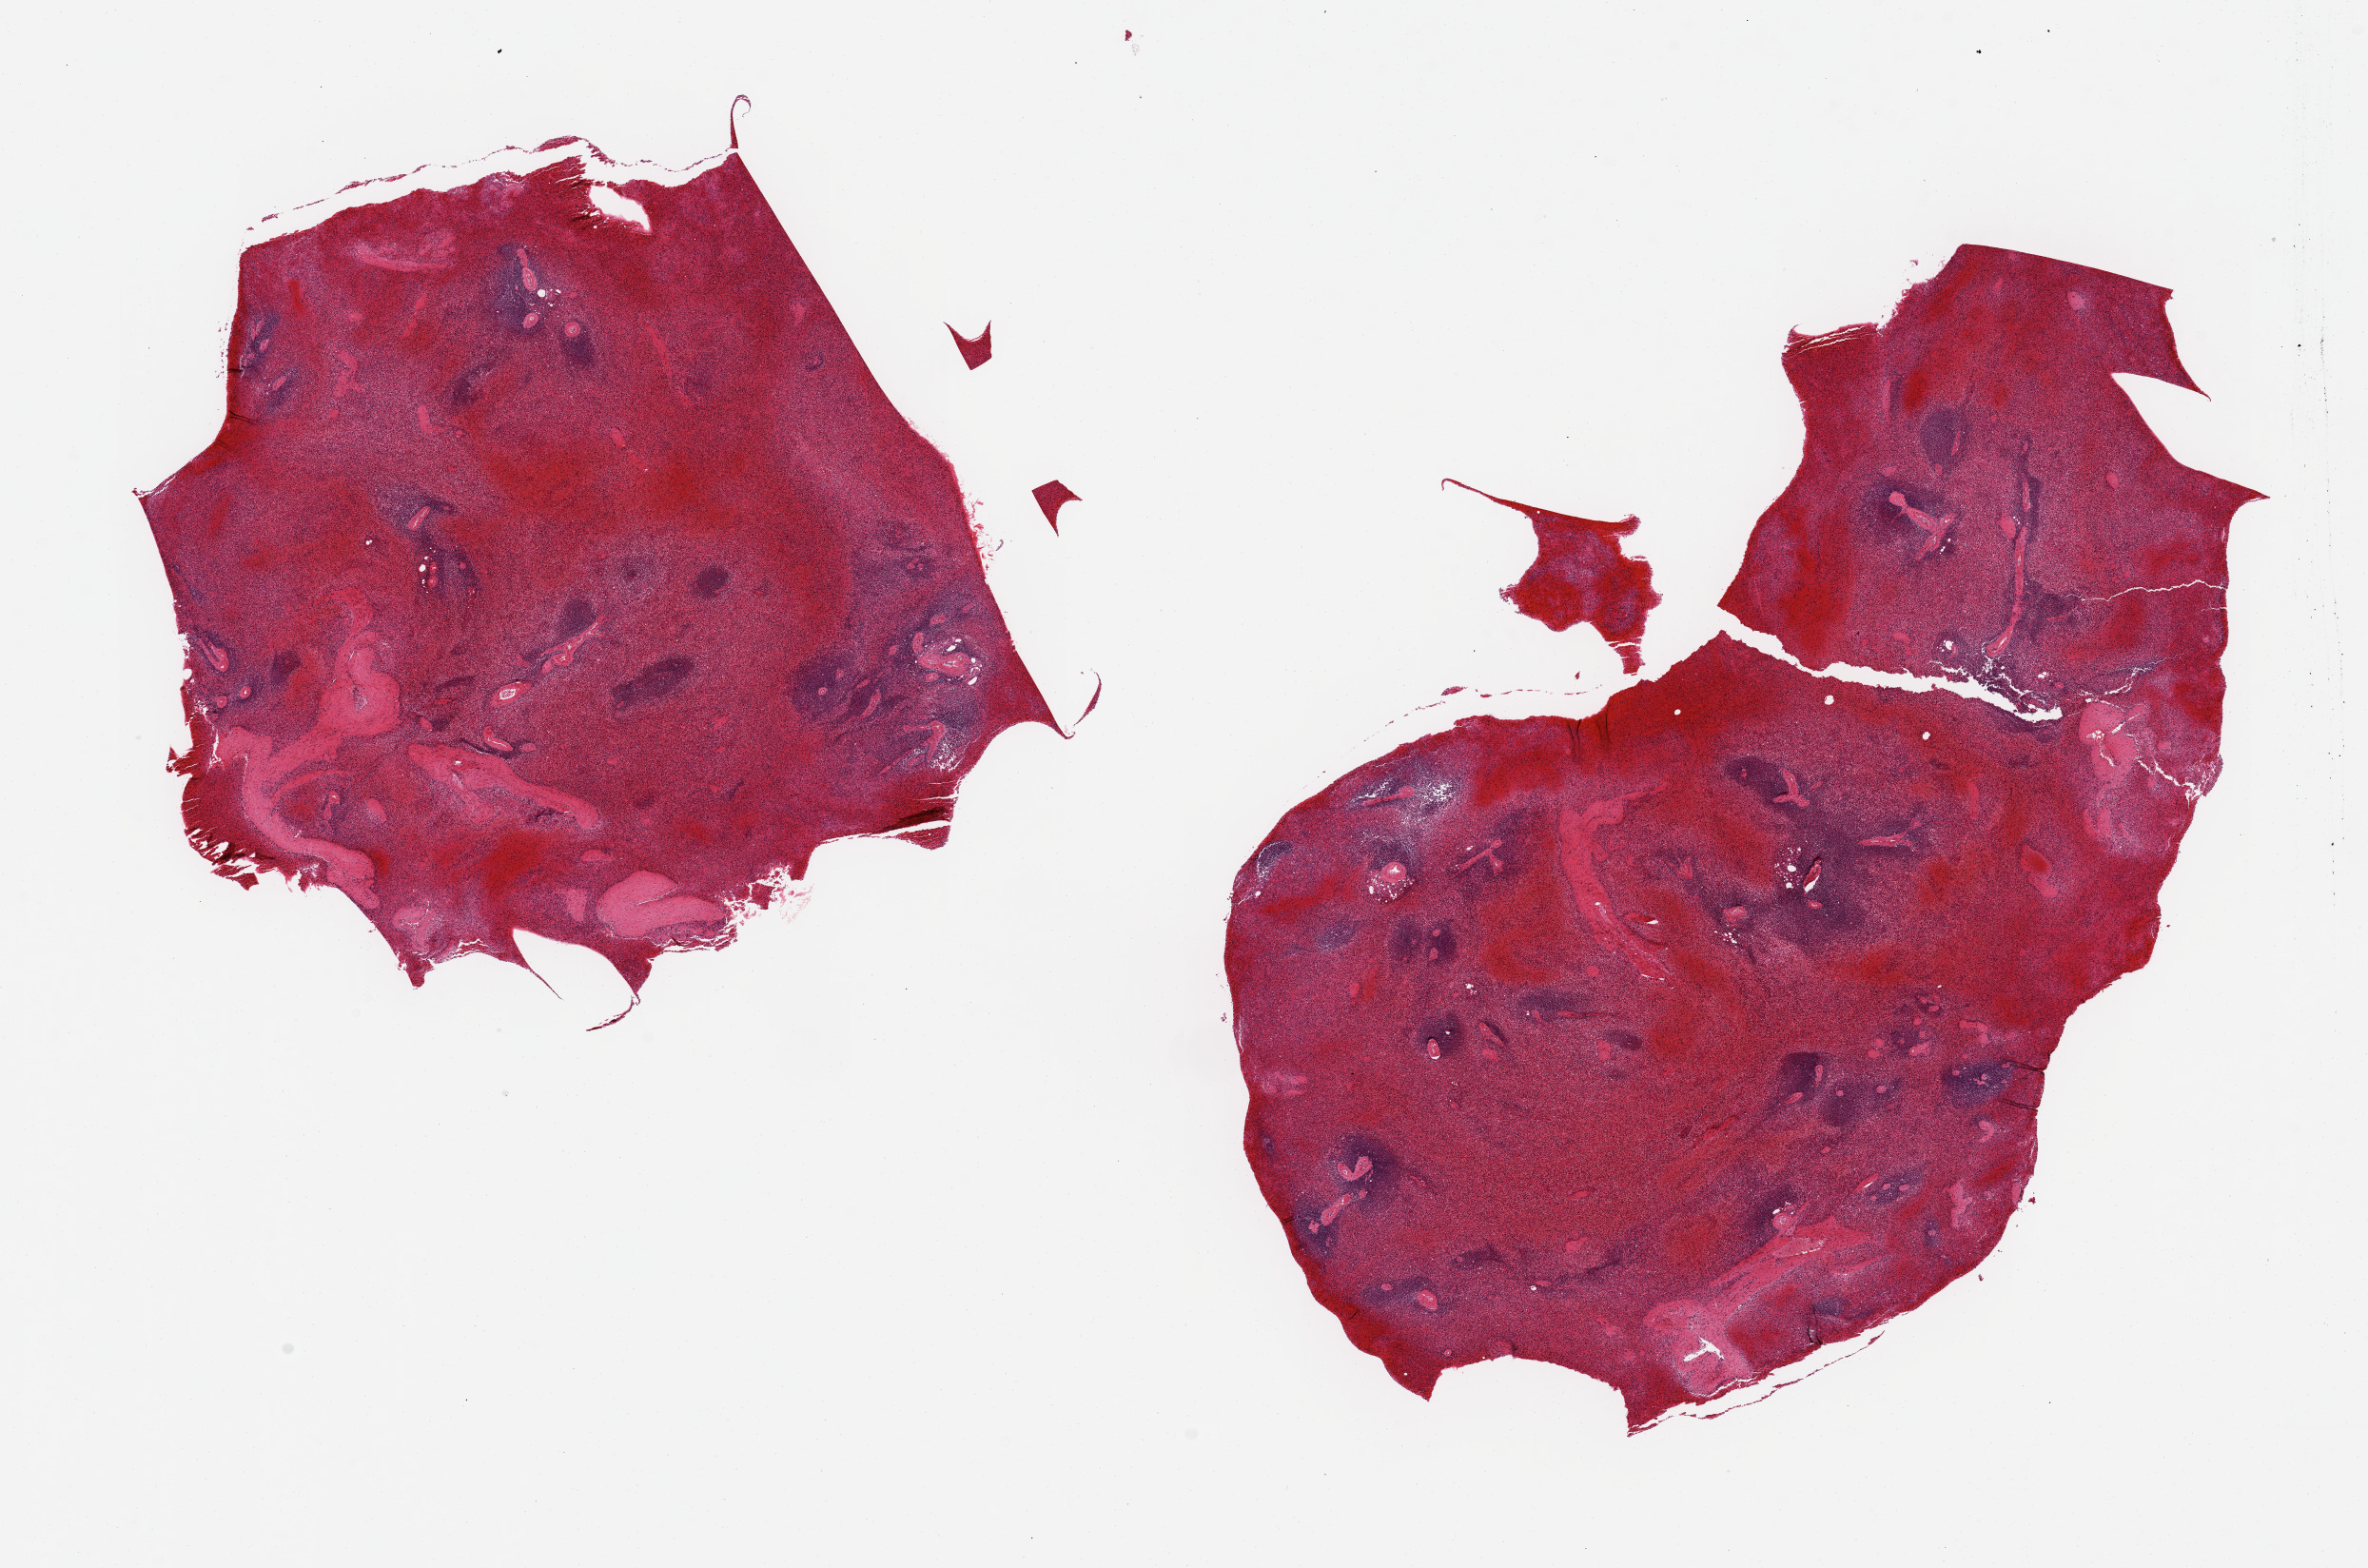
Hematoxylin and eosin (H&E) whole-slide image, shown as a low-resolution overview of the whole scanned area (about 19.7 x 13.0 mm), PAXgene-fixed paraffin-embedded (PFPE) section, sampled site (target tissue): spleen, donor tissue sample. Donor sex: male.
Reviewer comment on this tissue sample: 2 aliquots ~8x6mm. Congested.